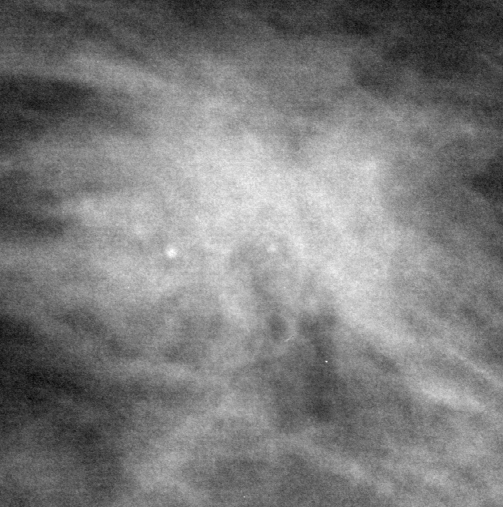
Crop from a digitized film mammogram around one marked abnormality, left breast, MLO view.
Marked abnormality: mass, shape irregular, margins spiculated; BI-RADS assessment category 5; pathology result (as recorded, not read from the image): malignant.